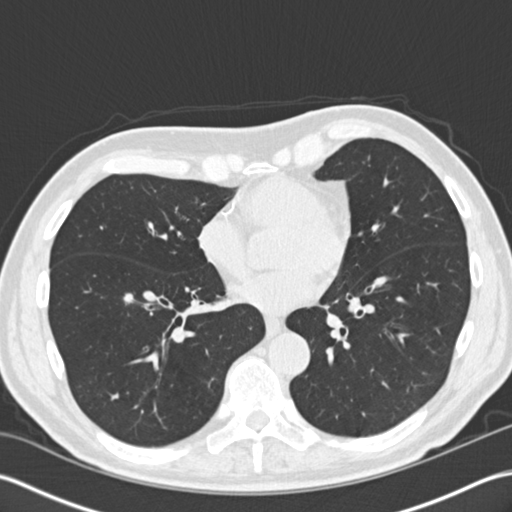
Low-dose screening chest CT, axial slice. First (baseline) screen. Lung window (W 1500 / L -600 HU). Standard (soft-tissue) reconstruction kernel (B30f). 512 × 512 image matrix, field of view 350 × 350 mm. Male participant, aged 73 years at enrolment. Former smoker at enrolment.
Expert reader's lesion annotation, bounding box <103,278,150,322> (left, top, right, bottom; pixels). No non-calcified nodule or mass ≥4 mm was recorded by the screening reader at this exam. Participant outcome: lung cancer diagnosed 430 days after this screen — non-small cell carcinoma, right lower lobe, stage IA (AJCC 6th edition), 30 mm at pathology.